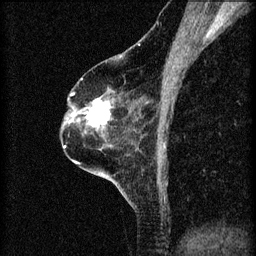
Breast MRI (dynamic contrast-enhanced), one sagittal slice; position 41 of 60 along the scan axis; 3 images stored at this slice position (order not interpretable as contrast timing); 1.5 T; TE 4.2 ms, TR 8.2 ms; 2 mm slice thickness; 256 × 256 image matrix. Patient: female, 60 years.
Outlined on this slice (semi-automatically segmented with operator editing):
- analysis volume of interest (the breast-tissue region the enhancement analysis was run in; not a lesion): bounding box (x1, y1, x2, y2) in pixels: (78, 94, 114, 131)
- tumour enhancement mask (voxels above the 70 % enhancement threshold inside the analysis volume of interest): (79, 98, 110, 125)